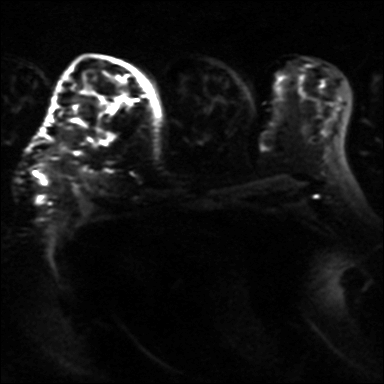
Breast MRI, one axial slice. Position 21 of 36 along the scan axis. Diffusion-weighted series; image 2 of 4 stored at this slice position (different b-values; order by instance number). 3 T. 4 mm slice thickness. 384 × 384 image matrix, field of view 320 × 320 mm. Female patient.
Annotated regions visible in this slice (outlined manually by an expert reader):
- tumour on diffusion-weighted imaging: box from (x=111, y=134) to (x=118, y=140) px